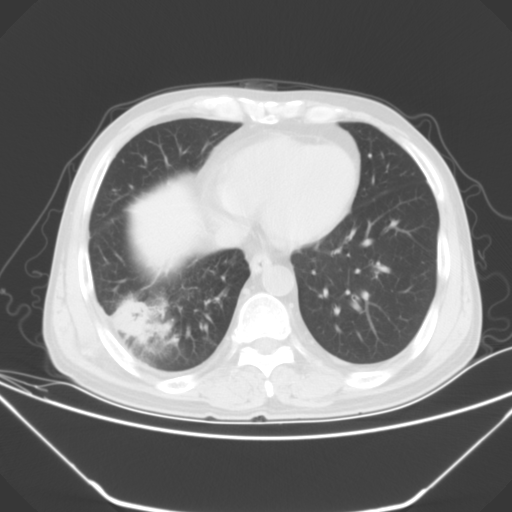
Chest CT, one axial slice; position 15 of 52 along the scan axis; 120 kVp; lung window (W 1500 / L -600 HU); 512 × 512 image matrix, field of view 379 × 379 mm. Male patient, age 54 years. From the clinical record (not read from this slice): clinical TNM (as recorded): T2 N1 M0; histopathological grade: G3.
Annotated regions visible in this slice (rectangle marked by the reading radiologist):
- lung tumour (recorded histology: adenocarcinoma): bounding box <112,300,149,339> (left, top, right, bottom; pixels)